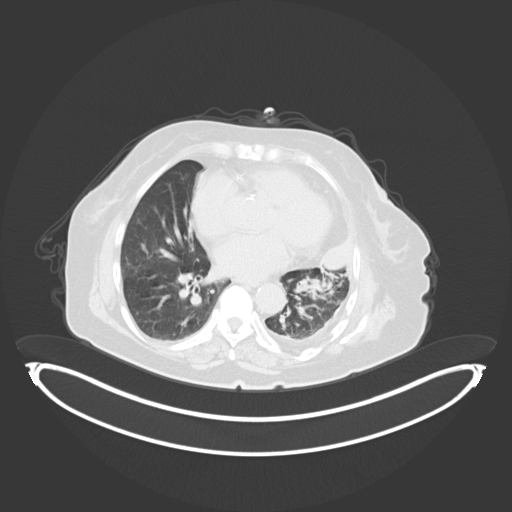
Chest CT, one axial slice; position 189 of 284 along the scan axis; 120 kVp; lung window (W 1500 / L -600 HU); 512 × 512 image matrix, field of view 500 × 500 mm. Female patient, age 75 years. Case-level facts recorded for this patient, not image findings: clinical TNM (as recorded): T3 N3 M1.
Outlined on this slice (bounding box drawn by a radiologist):
- lung tumour (recorded histology: adenocarcinoma): bounding box (x1, y1, x2, y2) in pixels: (315, 236, 356, 274)